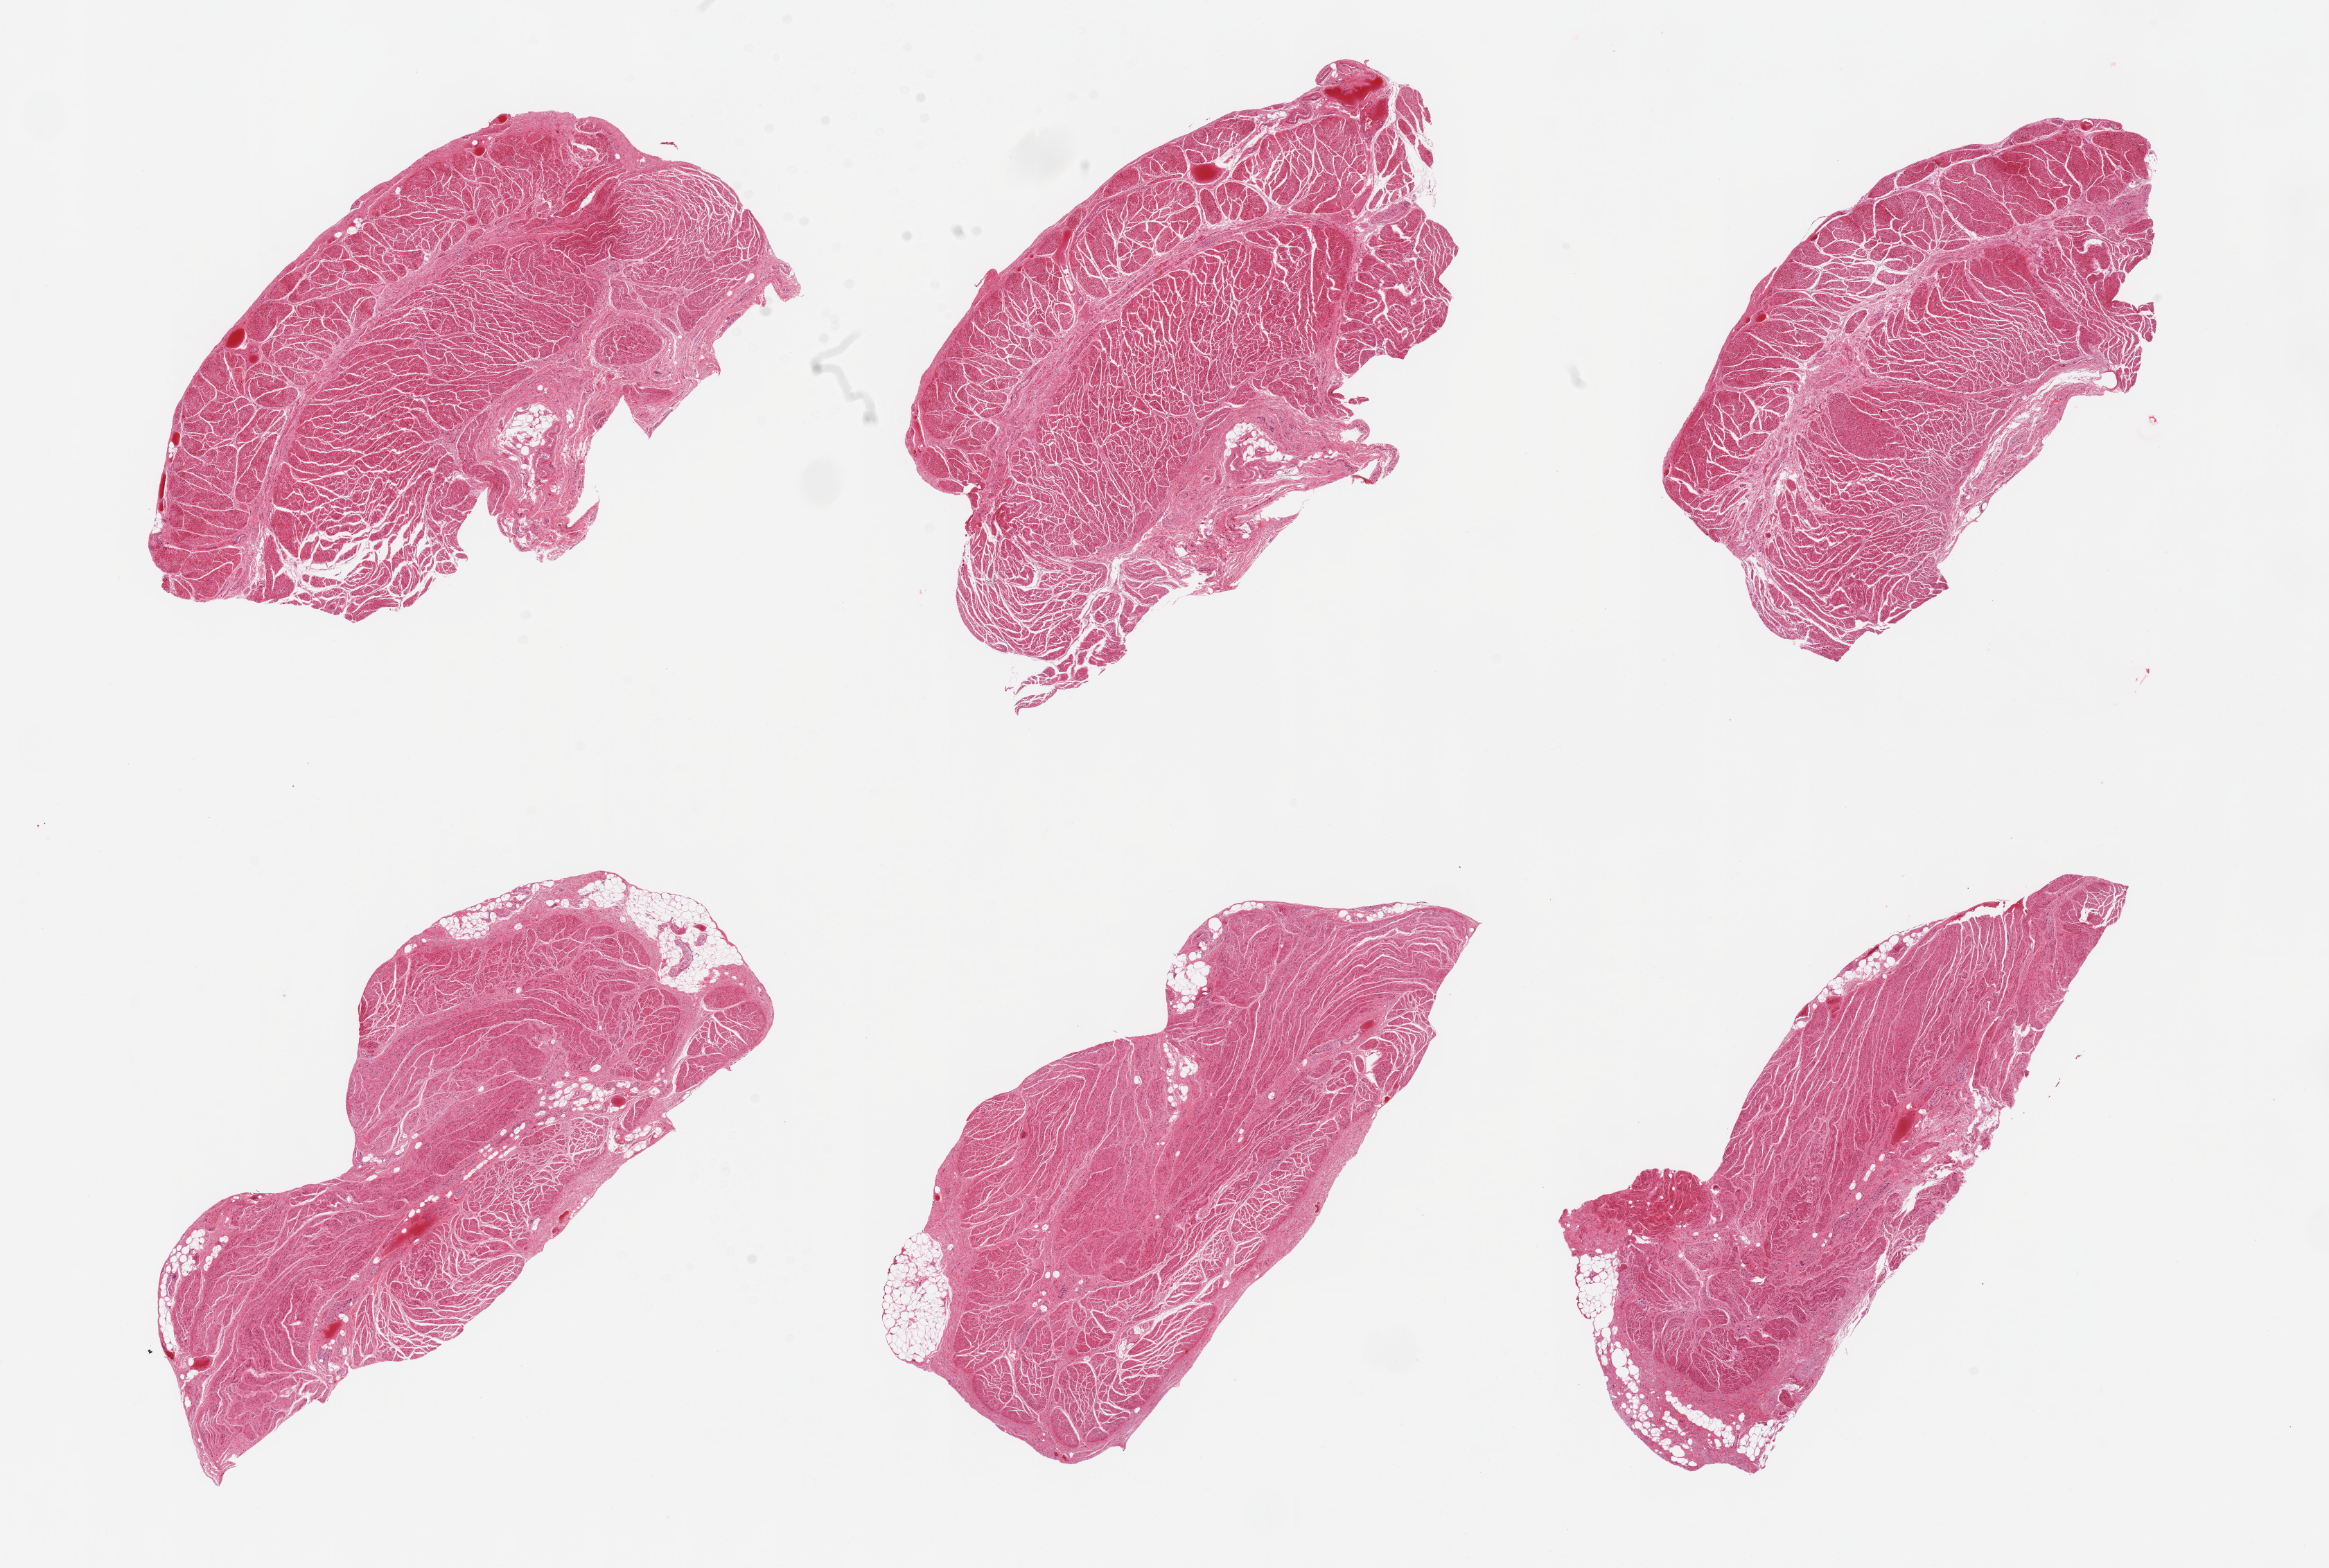
Whole-slide image, haematoxylin and eosin stain — low-resolution overview of the scanned area, about 26.6 x 17.9 mm (from a 20x scan). PAXgene-fixed paraffin-embedded (PFPE) section. Sampled site (target tissue): gastroesophageal junction. Tissue donor sample. Donor: male.
- pathologist's review note for this sample: 6 pieces; well trimmed, minimal residual fat/nerve